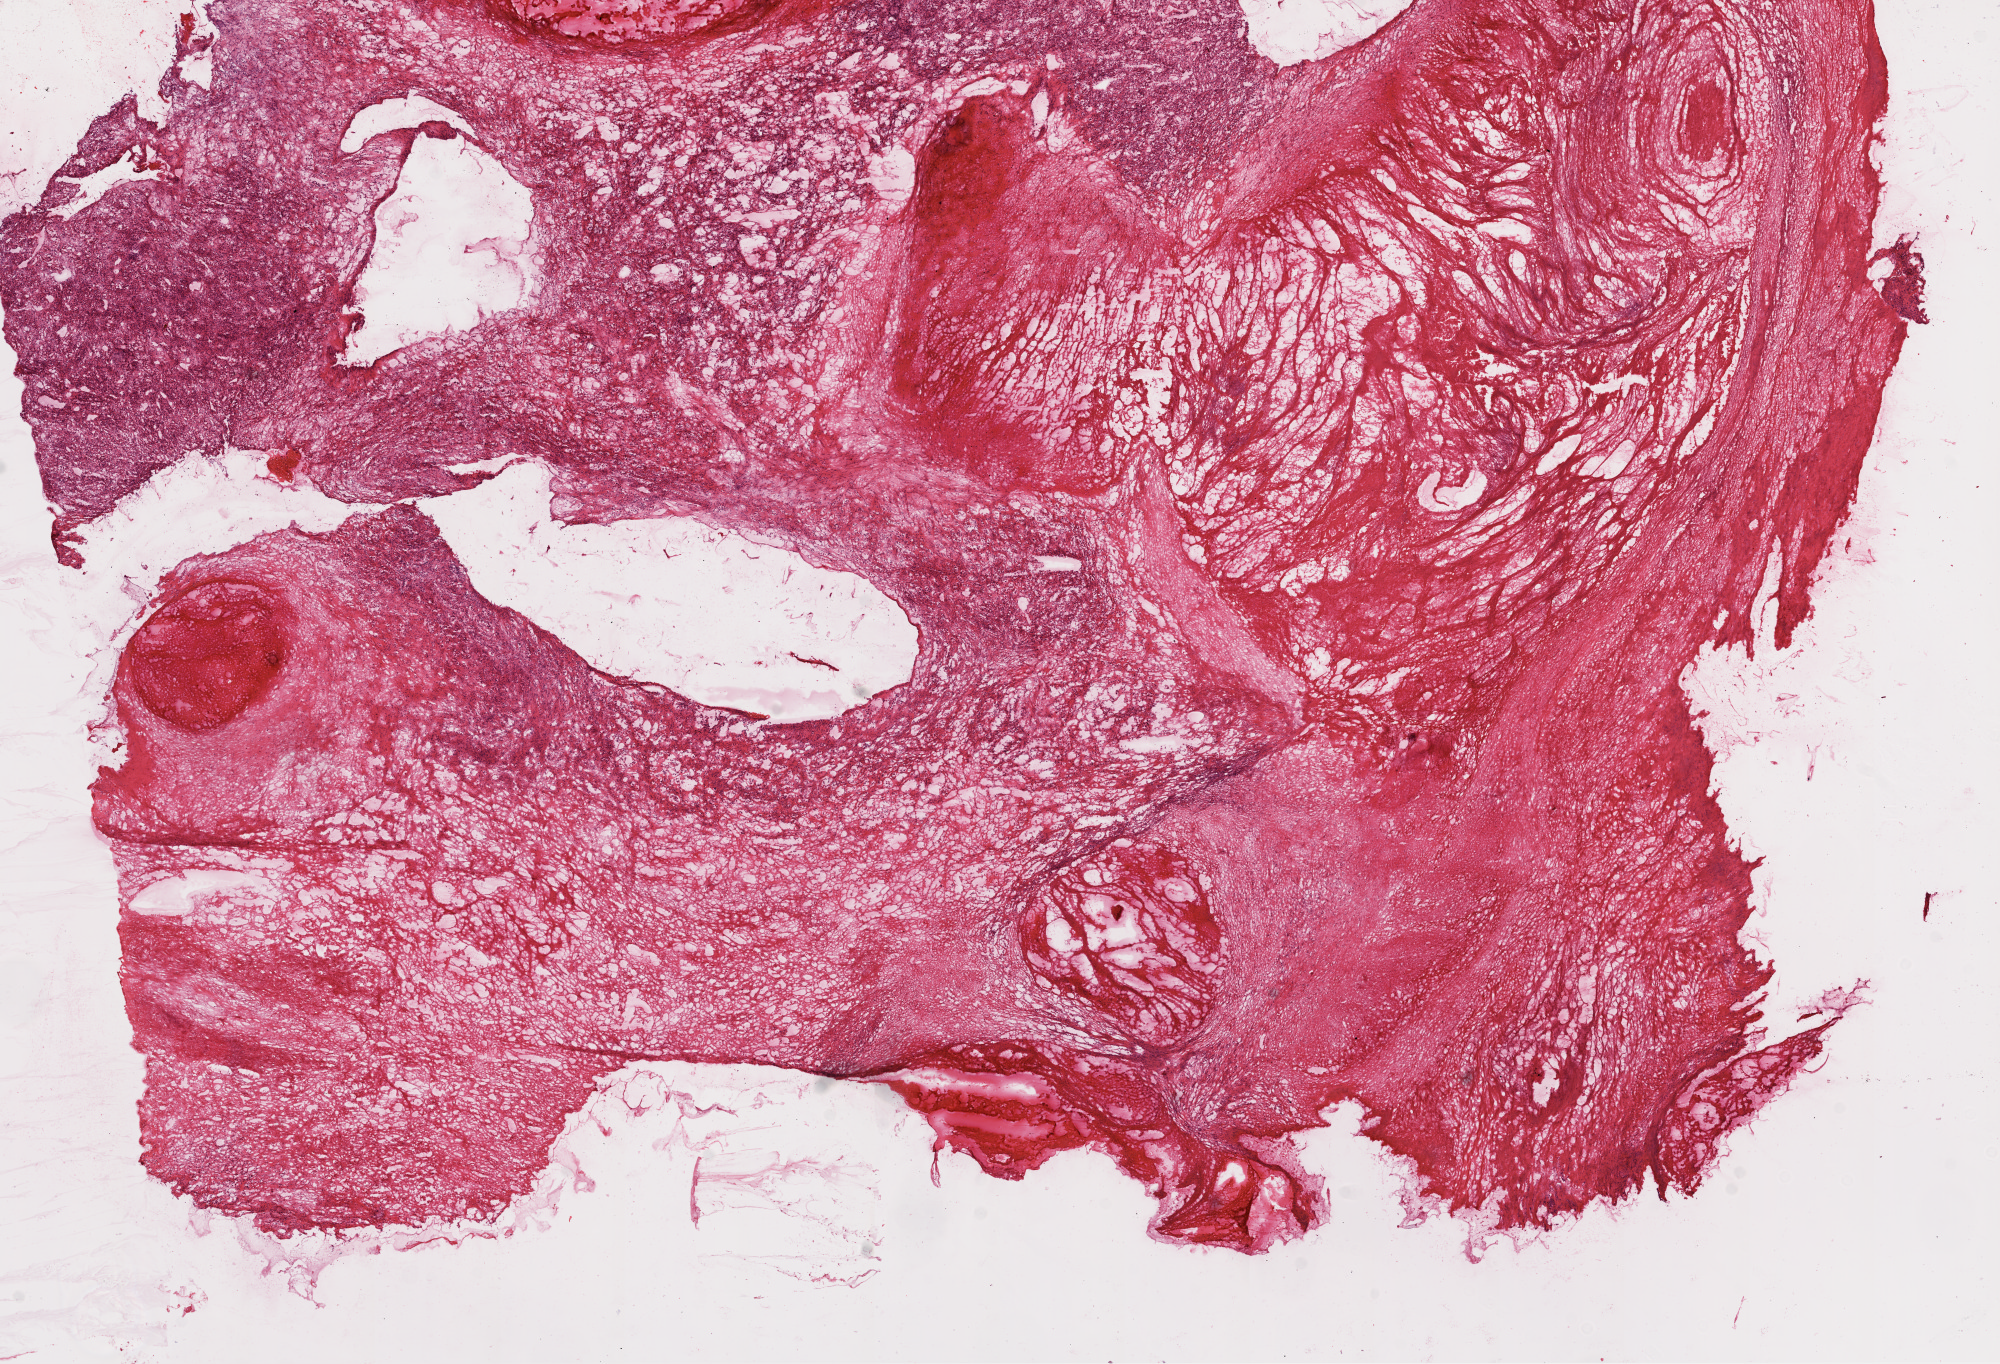
Digitized Hematoxylin and eosin (H&E) stained tissue section (whole slide), shown as a low-resolution overview of the whole scanned area (about 16.0 x 10.9 mm, slide scanned at 20x), frozen section, primary tumour sample from the kidney. Male patient; age at initial diagnosis 54 years. Histologic grade: G2 (moderately differentiated). Pathologist review of this section (percent, as recorded): tumour cells 50%, tumour nuclei 70%, normal cells 0%, stromal cells 50%, necrosis 0%.
• pathologic diagnosis: Clear cell adenocarcinoma, NOS
• TNM: T3a N0 M0
• AJCC pathologic stage: III (6th edition)